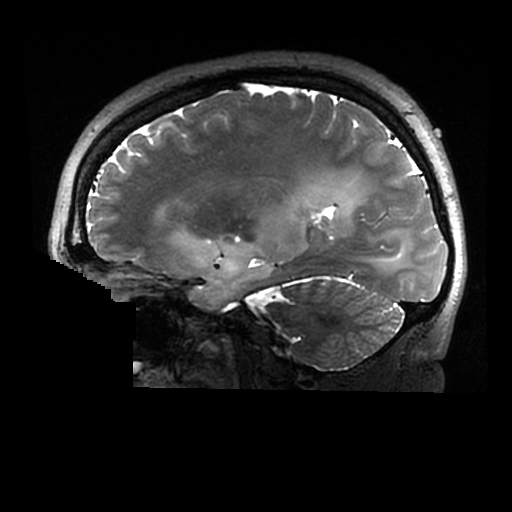
Brain MRI from a brain-tumour surgery series, one sagittal slice. Slice 184 of 320 in the series (ordered by position). 0.6 mm slice thickness. 512 × 512 image matrix, field of view 240 × 240 mm. Case-level facts recorded for this patient, not image findings: histopathology: Astrocytoma; WHO grade: 2; IDH mutation: yes.
Annotated regions visible in this slice (expert manual segmentation):
- tumour: bounding box [x1, y1, x2, y2] px = [174, 183, 406, 310]